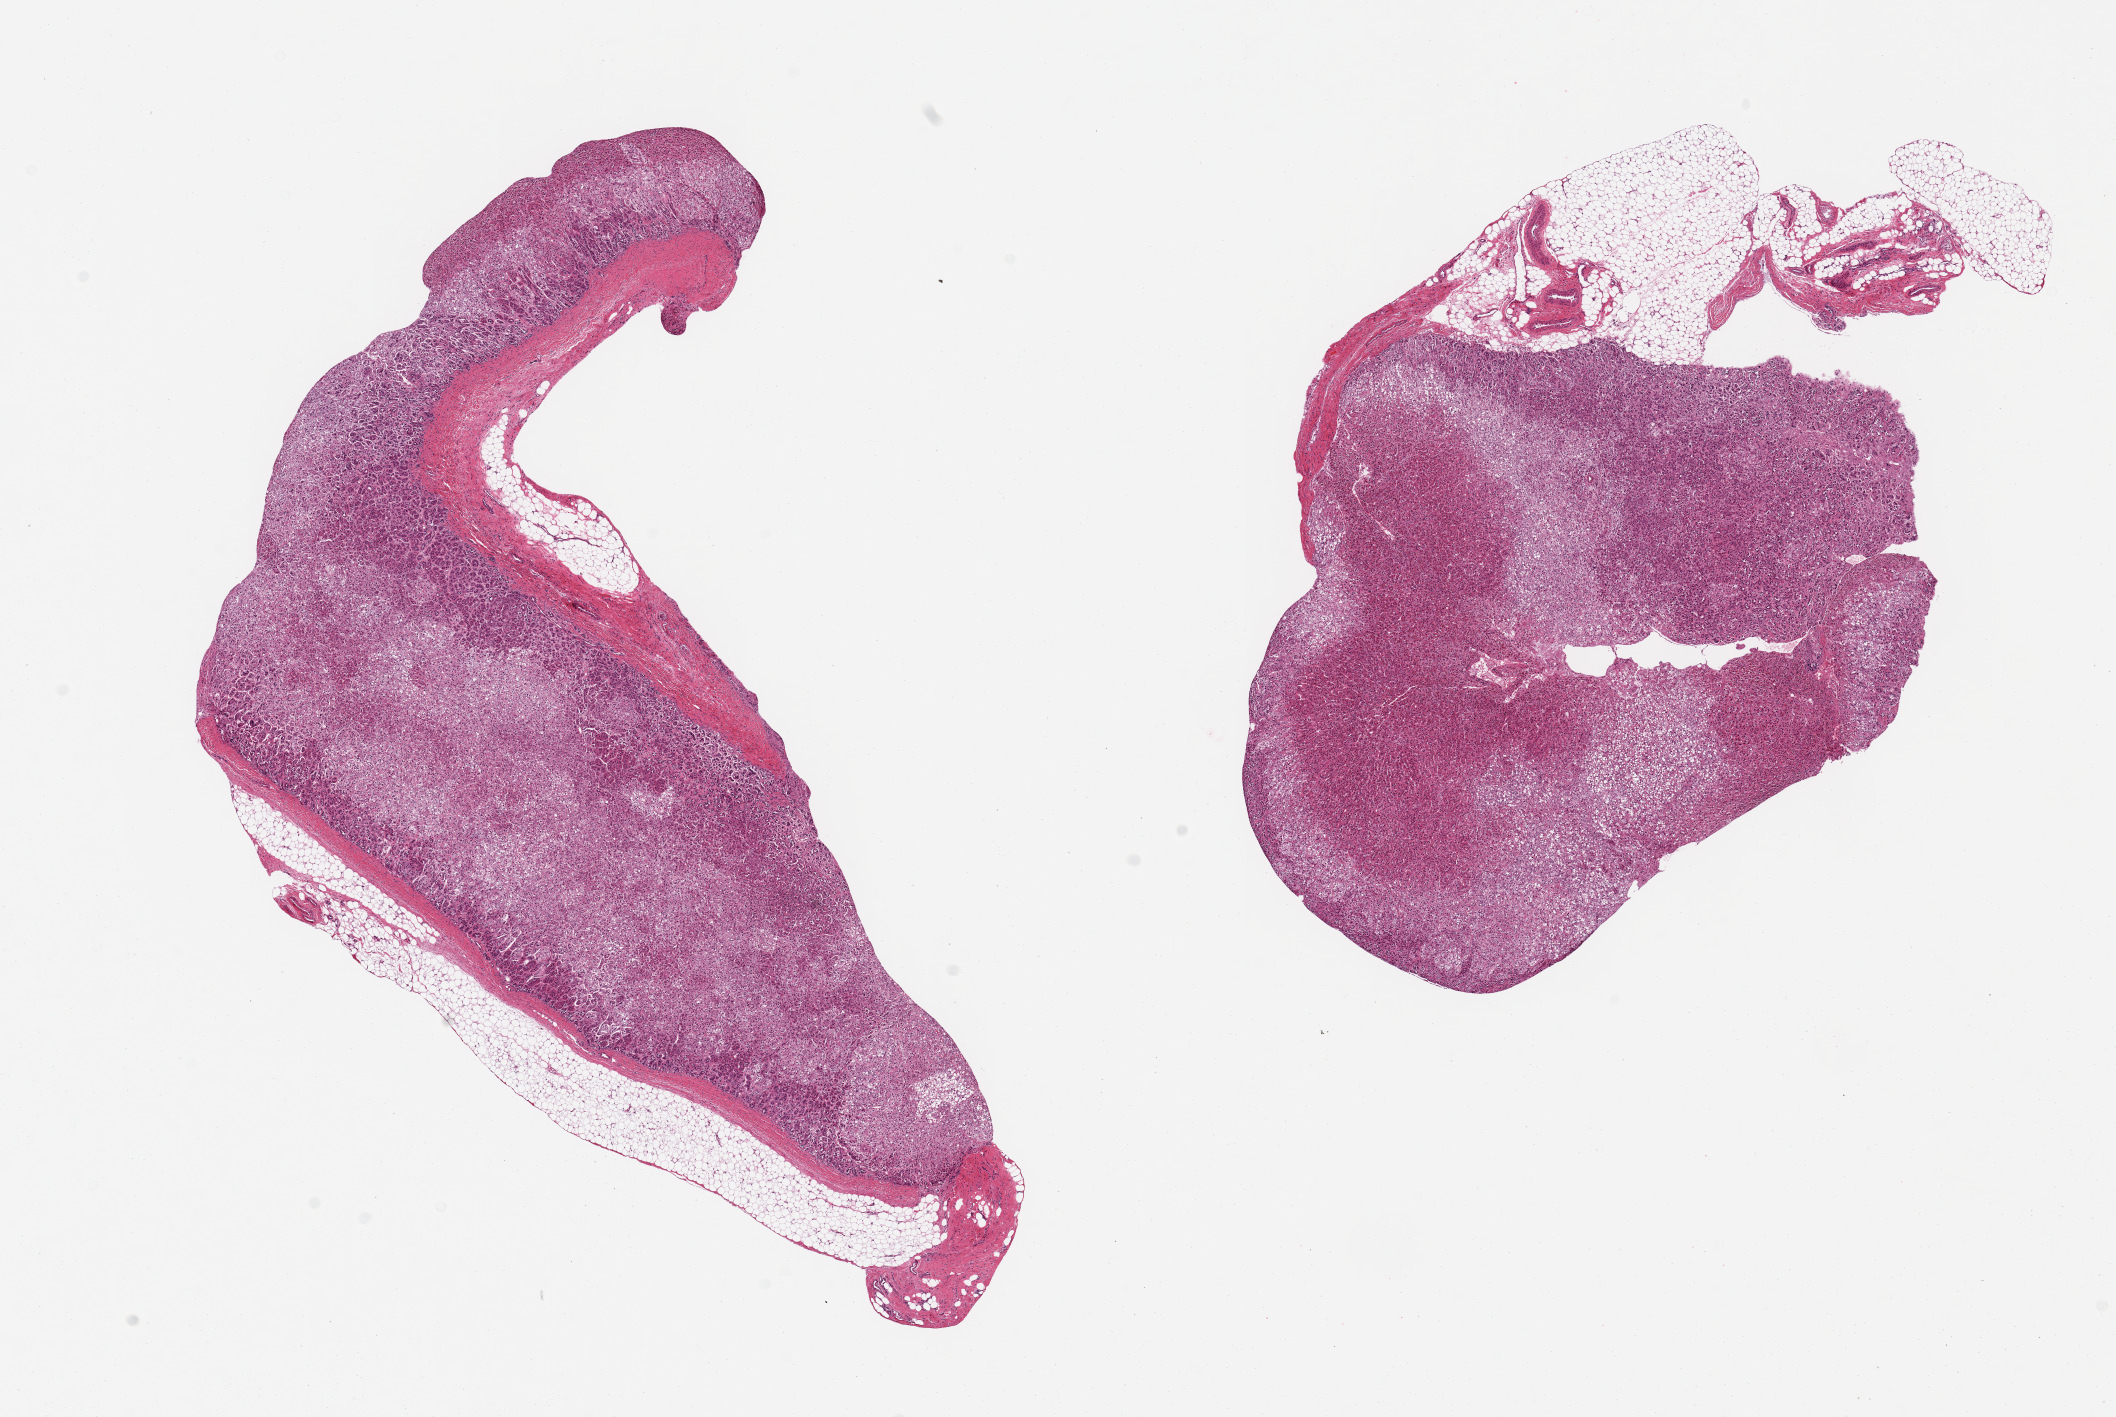
H&E whole-slide image — low-resolution overview of the scanned area, about 16.7 x 11.2 mm; PAXgene-fixed, paraffin-embedded tissue; section of adrenal gland (target tissue); donor tissue sample. Female donor.
Pathologist's review note for this sample: 2 pieces; well preserved cortex; 20 & 30% adherent fat.